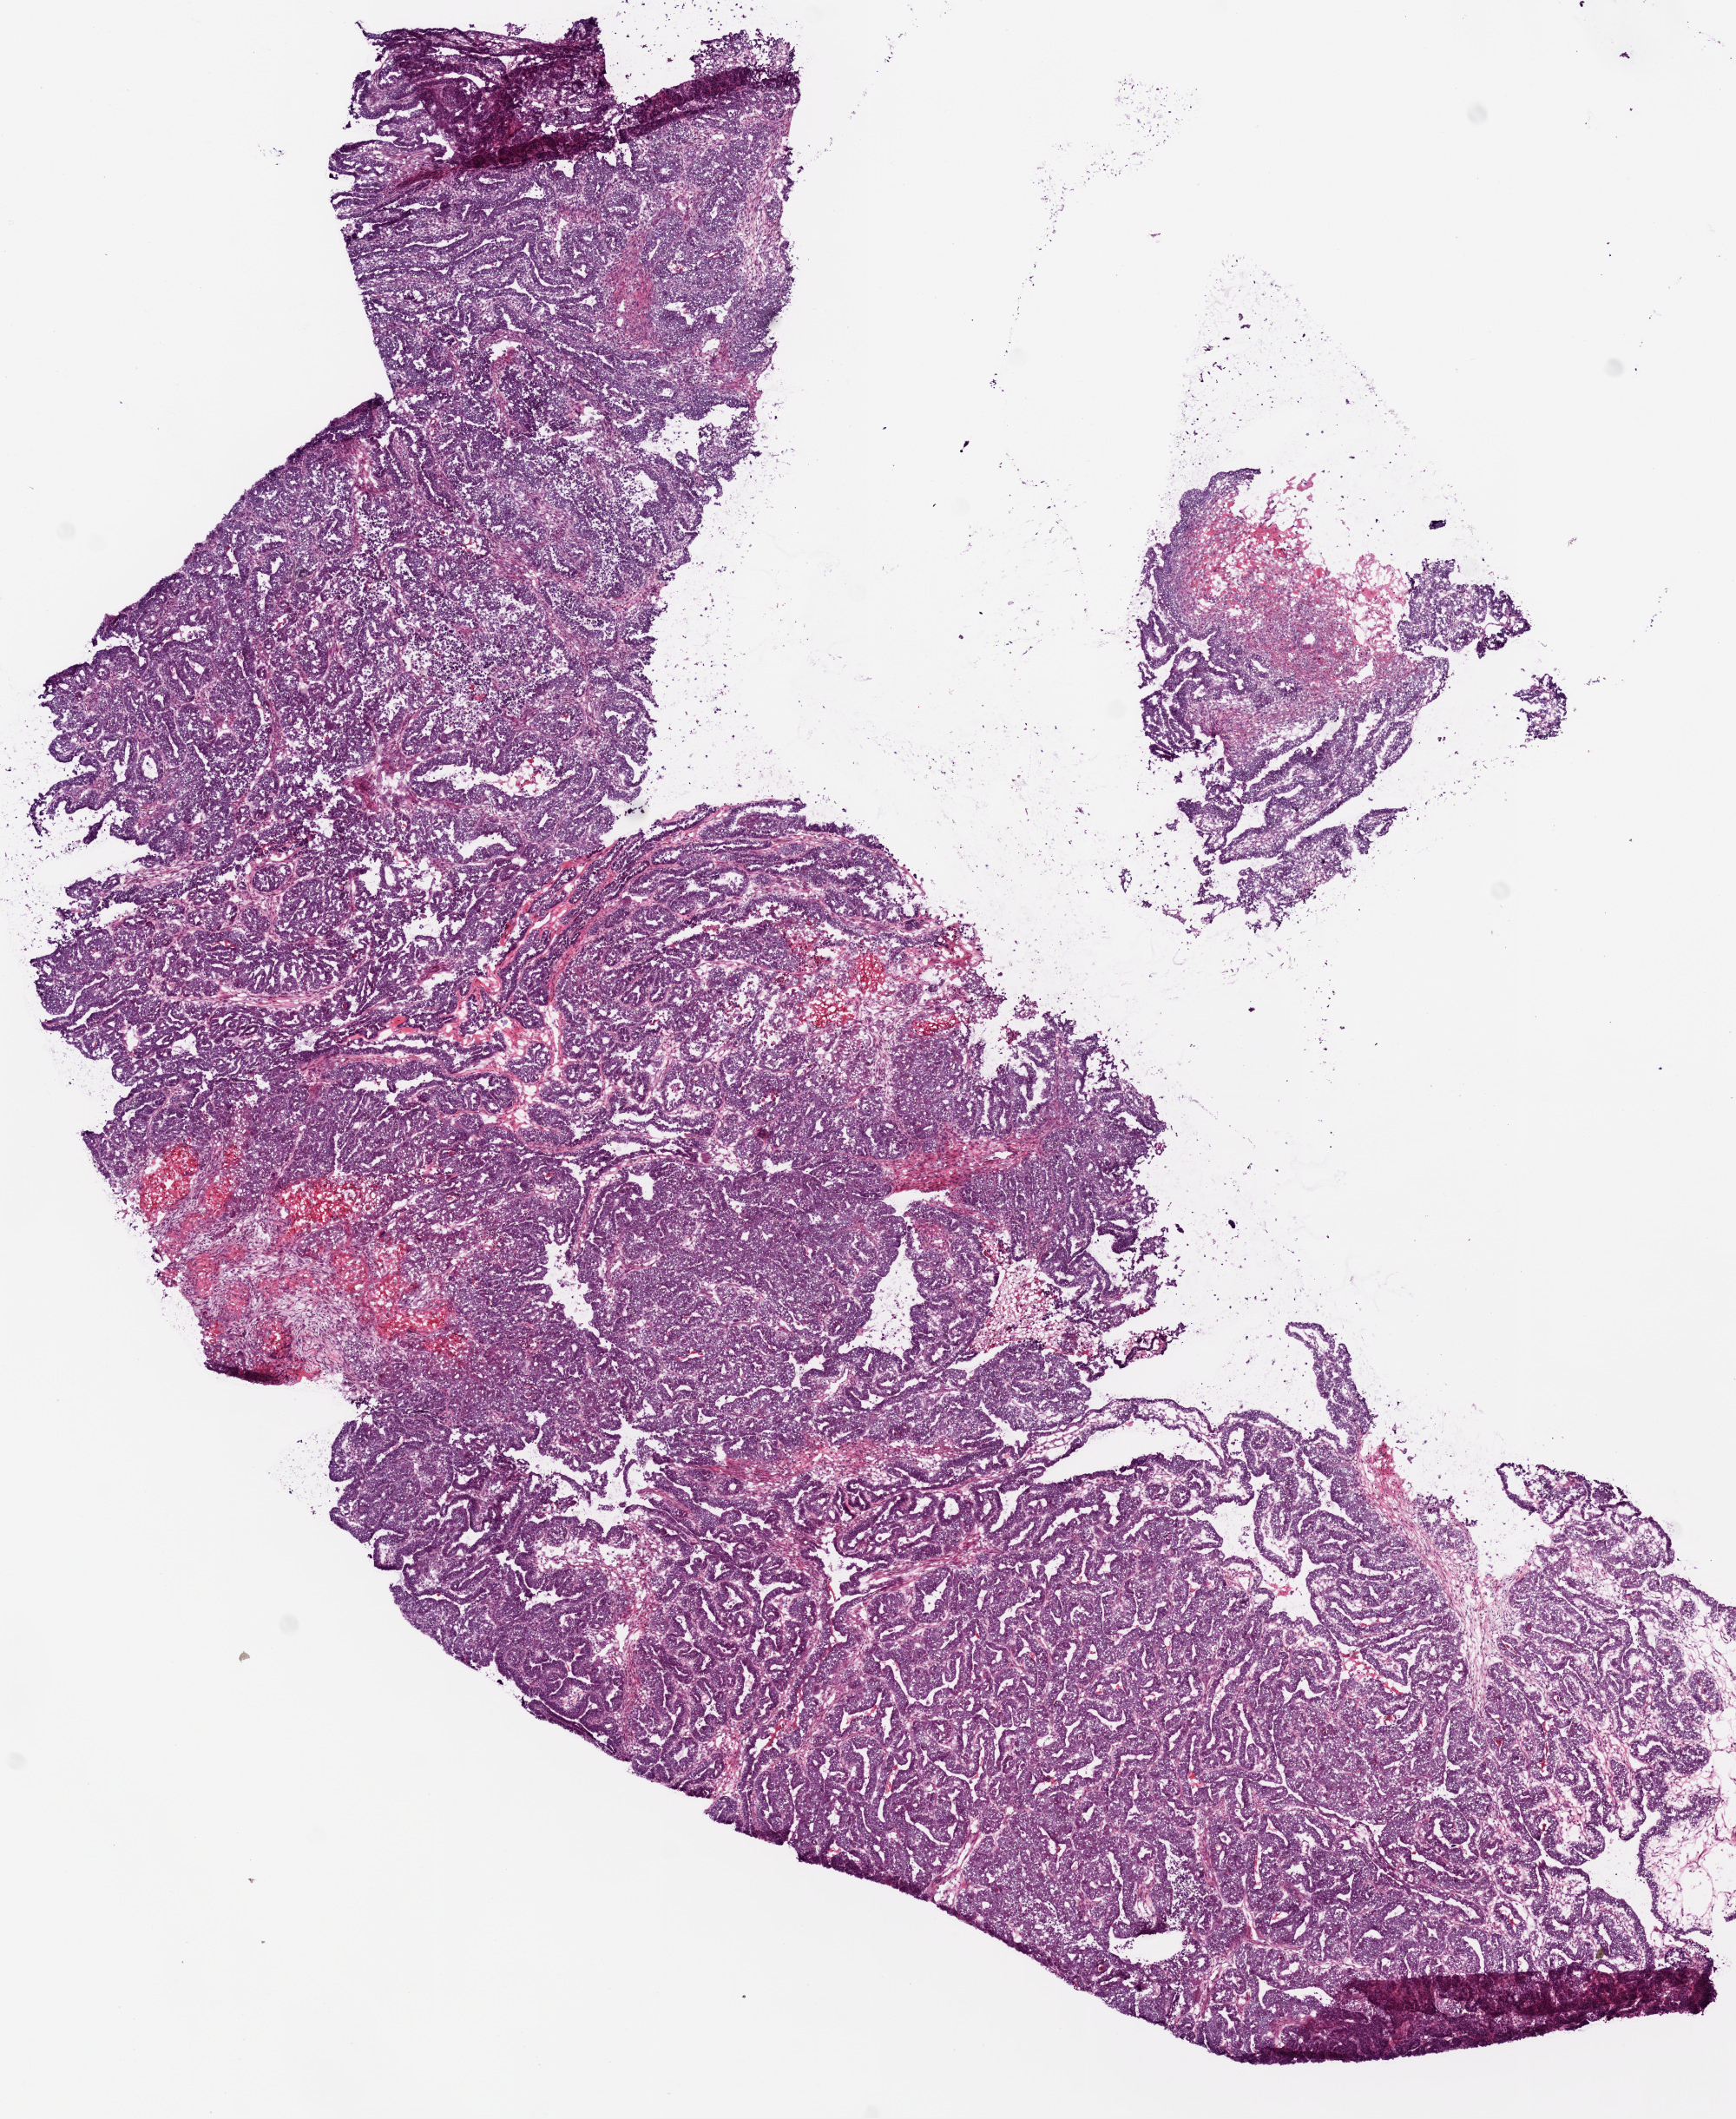
H&E-stained whole-slide image — shown as a low-resolution overview of the whole scanned area (about 8.0 x 9.8 mm). Frozen section from the bottom of the tissue portion. Sample: primary tumour, ovary. Patient: female, age at initial diagnosis 54 years. Histologic grade: G3 (poorly differentiated). Pathologist review of this section (percent, as recorded): tumour cells 94%, tumour nuclei 95%, normal cells 0%, stromal cells 5%, necrosis 1%.
- diagnosis: Serous cystadenocarcinoma, NOS
- laterality: bilateral
- FIGO stage: IIIB